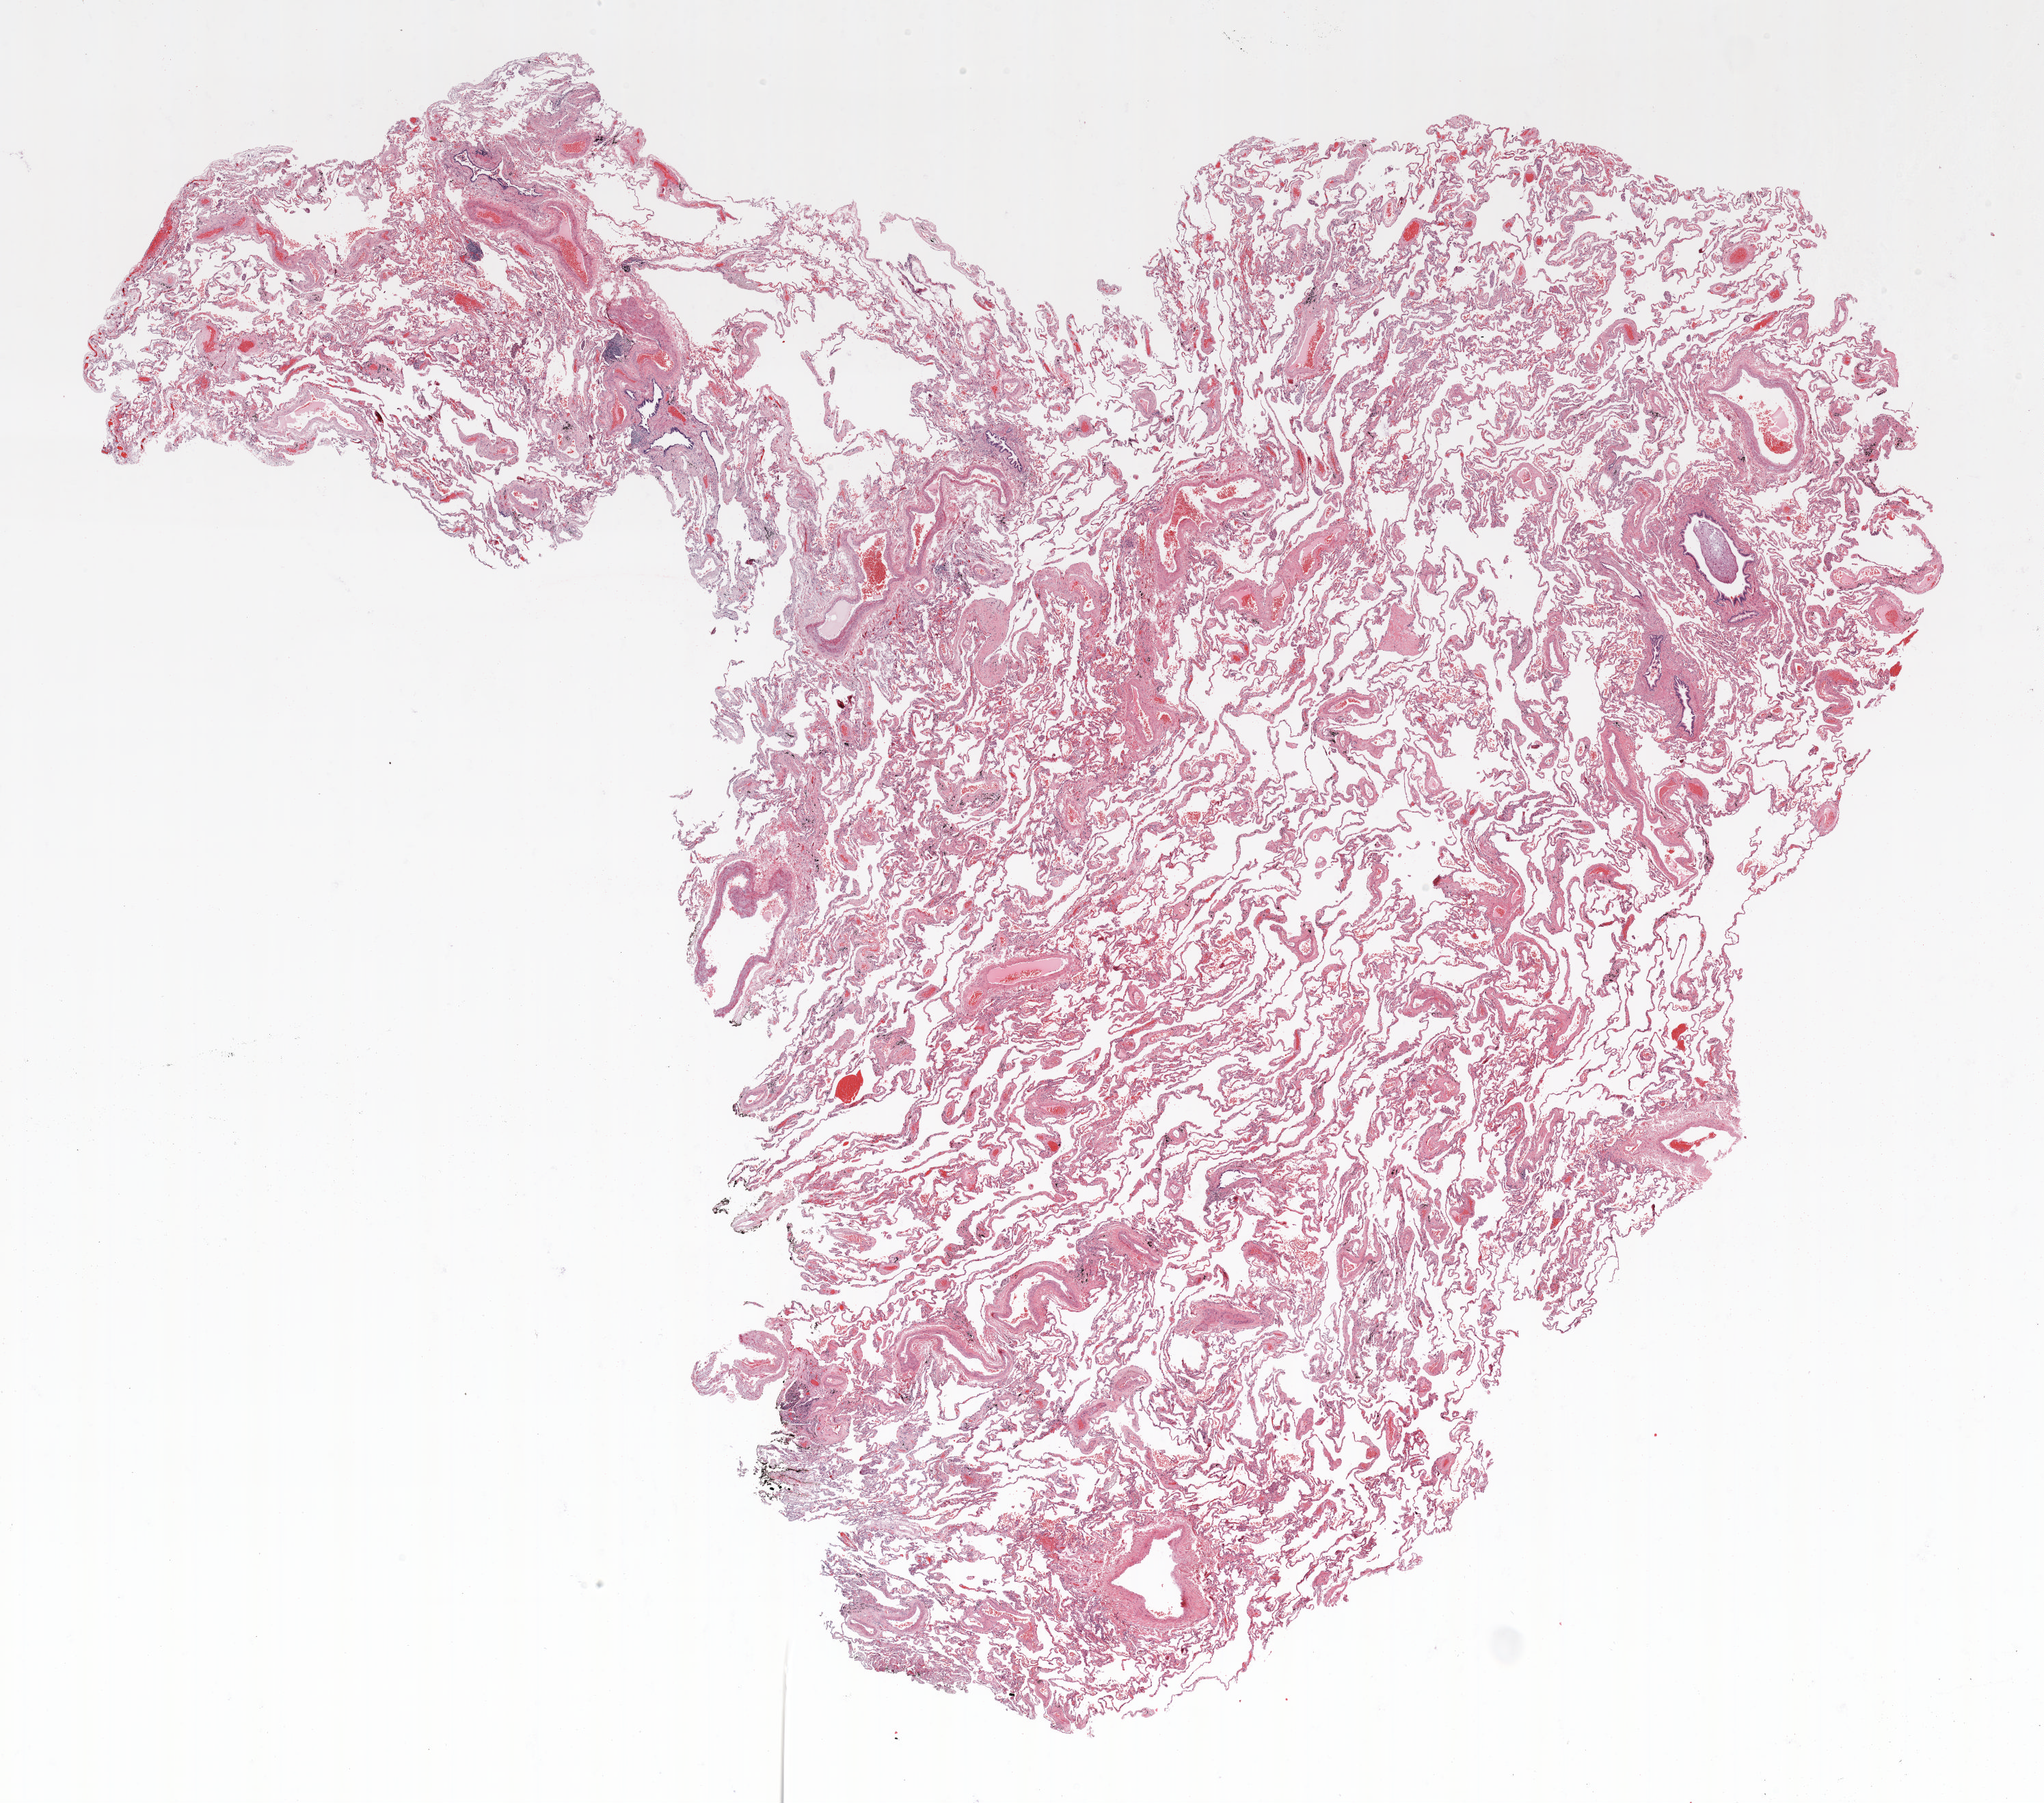
Whole-slide histology image, H&E-stained, a low-resolution overview of the entire scanned area, about 24.0 x 21.2 mm; formalin-fixed paraffin-embedded (FFPE) section; lung tissue. Female, age 62 at enrolment. Former smoker at enrolment. Grade: well differentiated (G1).
Participant's lung-cancer diagnosis: Adenocarcinoma, NOS (ICD-O-3 8140/3). Primary tumour location (clinical record): right upper lobe. Tumour size (pathology): 7 mm. Stage (AJCC 6th edition): IA.